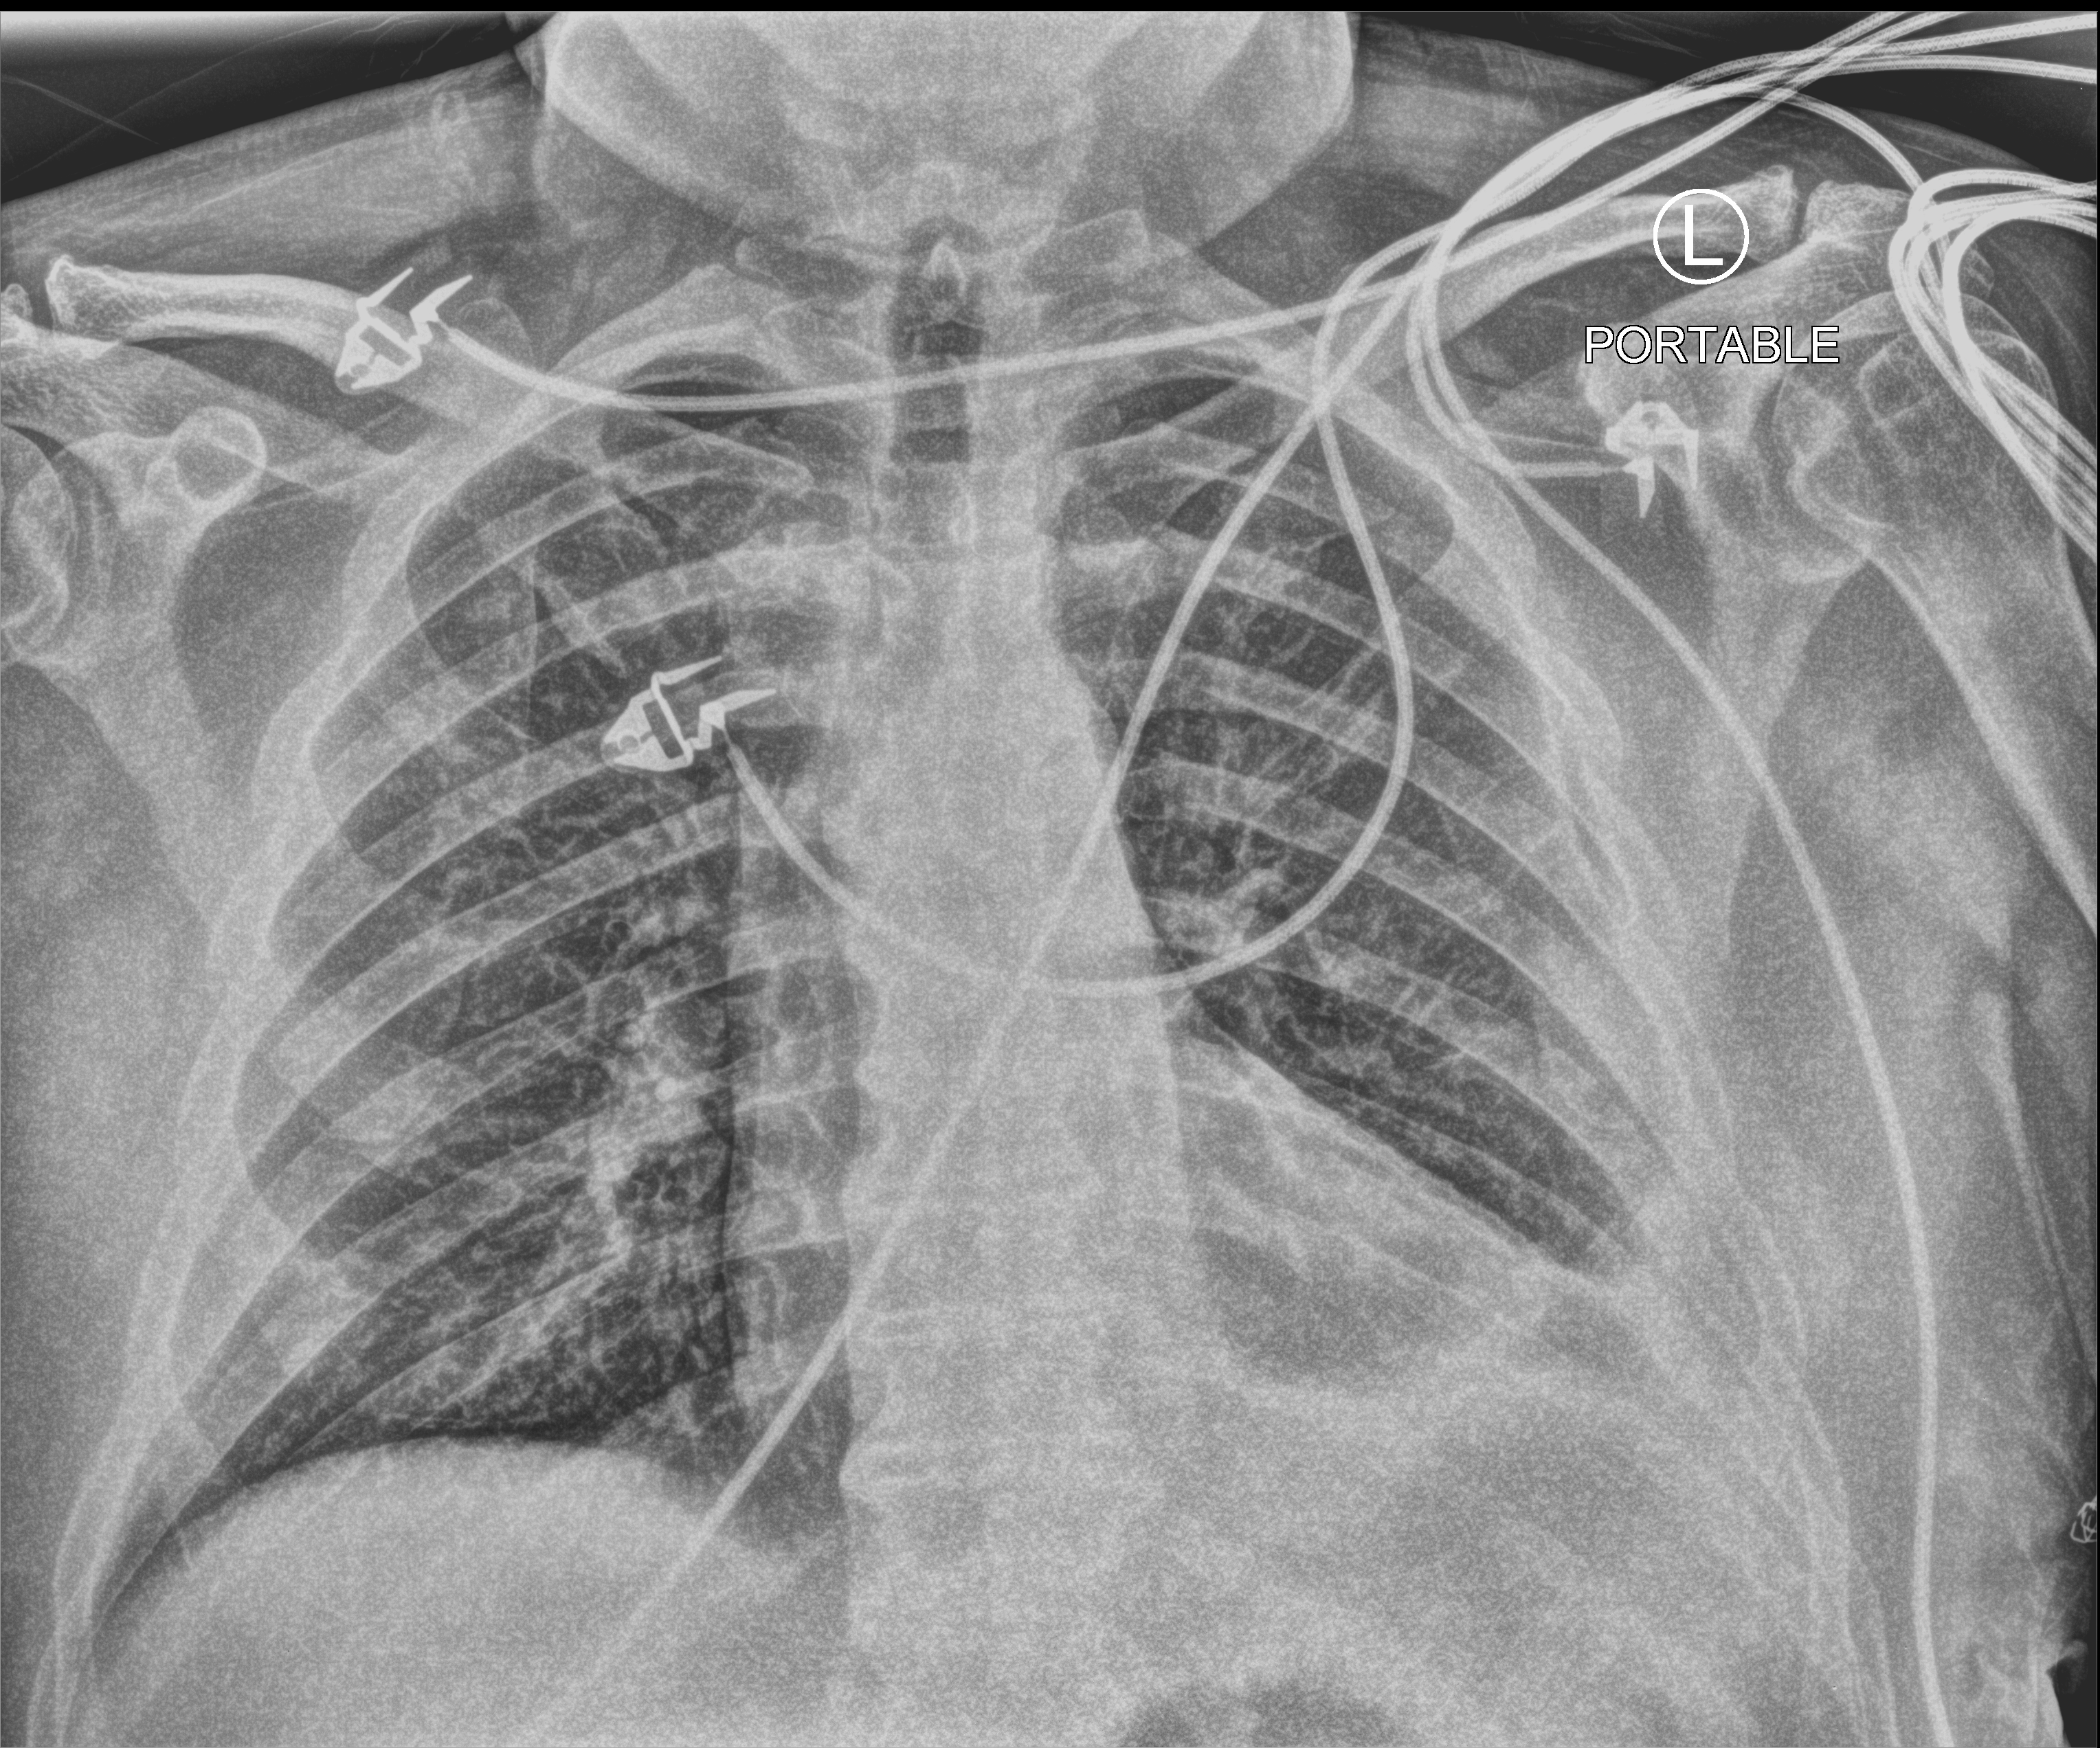
Bedside chest radiograph (computed radiography). Male patient hospitalised with COVID-19, age 18–59 years.
Admission-level facts for this patient (not findings on this image; timing relative to this image not recorded): admitted to intensive care during this hospital stay: no.